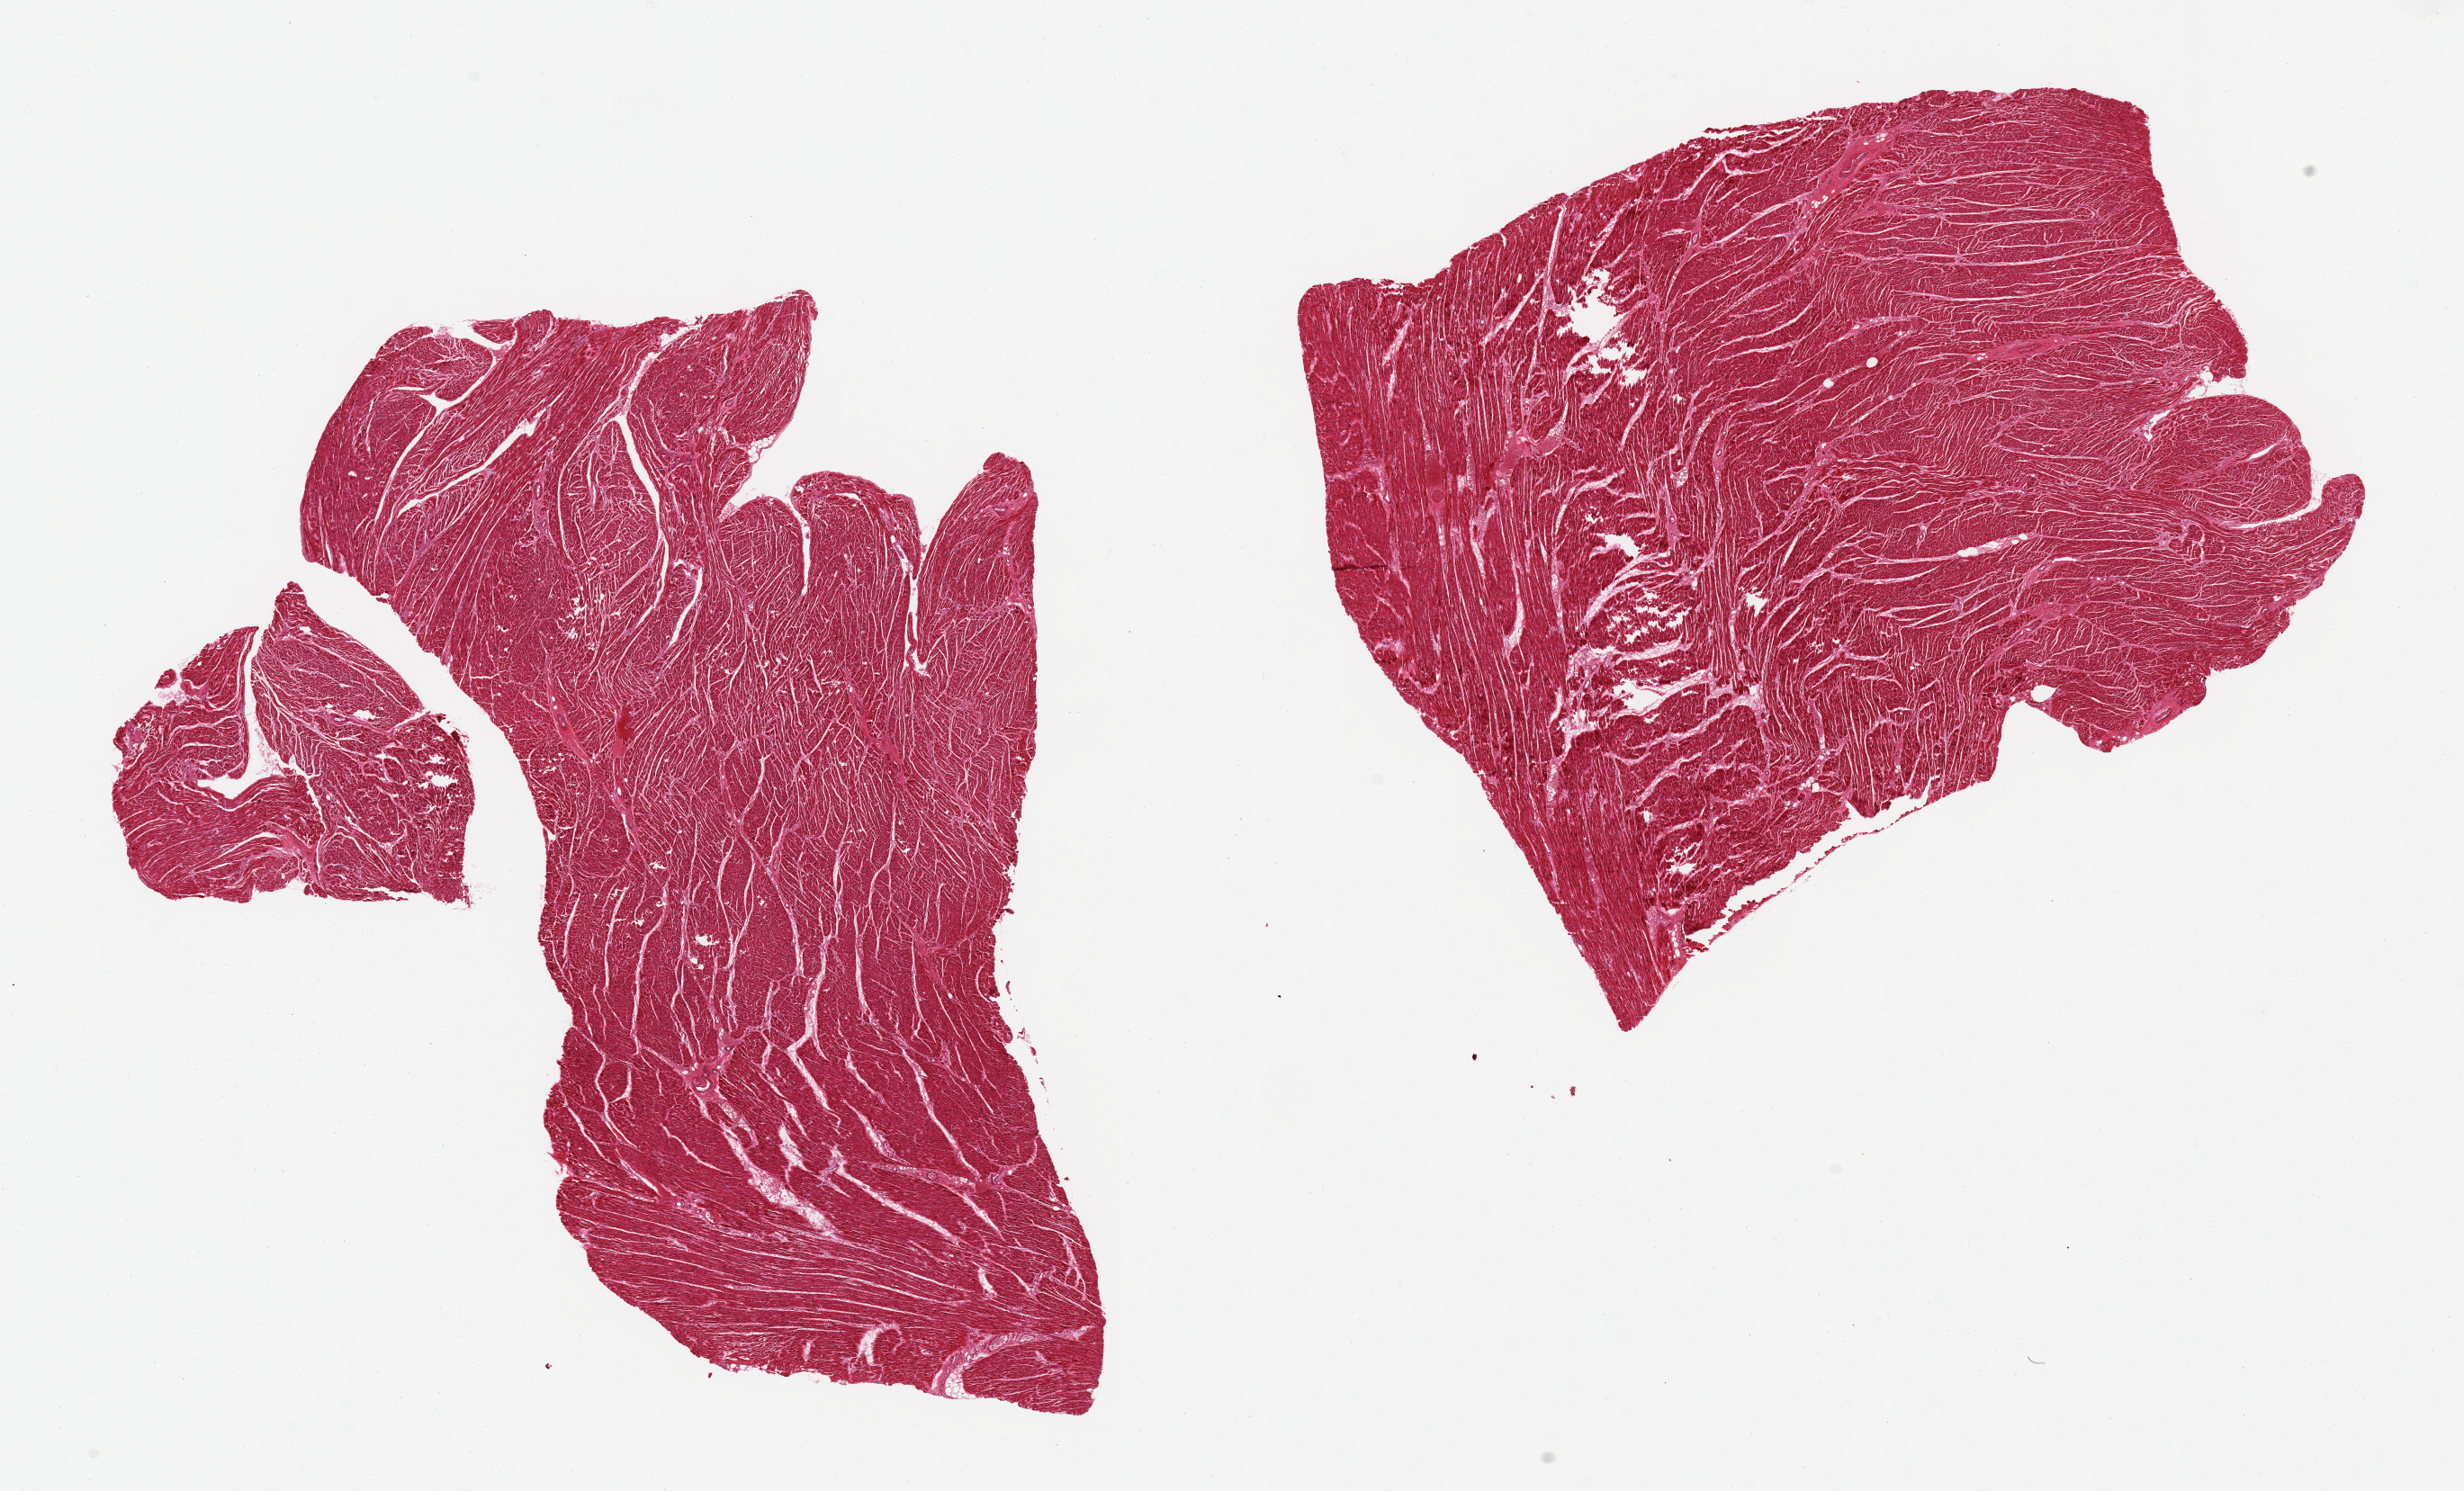
Haematoxylin and eosin whole-slide image — shown as a low-resolution overview of the whole scanned area (about 21.7 x 13.1 mm), PAXgene-fixed paraffin-embedded (PFPE) section, target tissue: heart, tissue donor sample.
Pathologist's review note for this sample: 2 pieces, 8x6 & 8x6 mm.